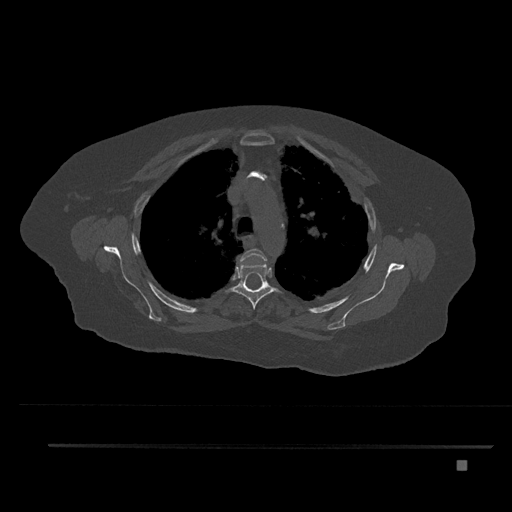
CT including the spine, one axial slice. Position 606 of 797 along the scan axis. Reconstruction kernel Br40s/3. Bone window (W 1800 / L 400 HU). 0.5 mm slice thickness. 512 × 512 image matrix, field of view 437 × 437 mm. Female patient, age 76 years. Case-level facts recorded for this patient, not image findings: primary cancer: lung; vertebrae with lytic lesions (as recorded): T11, L3.
Outlined on this slice (semi-automatically segmented with operator editing):
- T3 vertebra: bounding box (x1, y1, x2, y2) in pixels: (240, 248, 267, 264)
- T4 vertebra: (227, 257, 281, 309)